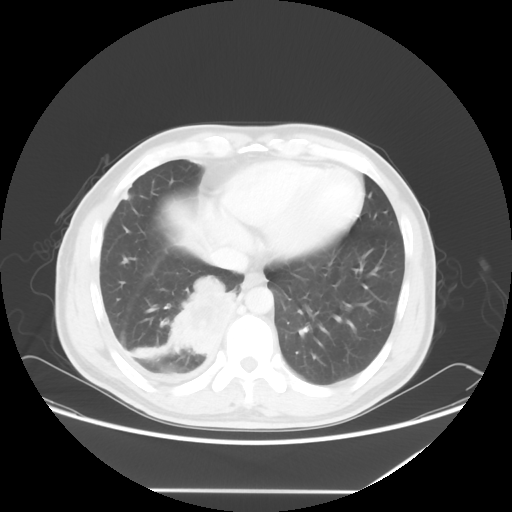
Chest CT, one axial slice; position 19 of 60 along the scan axis; 120 kVp; lung window (W 1500 / L -600 HU); 512 × 512 image matrix, field of view 419 × 419 mm. Patient: male, 48 years. Case-level facts recorded for this patient, not image findings: clinical TNM (as recorded): T3 N3 M1a.
Structures marked on this image (rectangle marked by the reading radiologist):
- lung tumour (recorded histology: squamous cell carcinoma): bounding box [x1, y1, x2, y2] px = [165, 271, 241, 361]